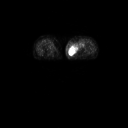
FDG PET of an extremity soft-tissue mass (from a PET/CT study), one axial slice; 128 × 128 image matrix. Patient: female, 74 years. From the clinical record (not read from this slice): histological type: pleomorphic leiomyosarcoma; grade: high; site of the primary tumour: left thigh.
Annotated regions visible in this slice (expert contour drawn on MRI and transferred to this co-registered scan by the dataset authors):
- gross tumour volume including surrounding oedema: bounding box (x1, y1, x2, y2) in pixels: (69, 41, 85, 55)
- gross tumour volume (mass): (69, 46, 77, 55)